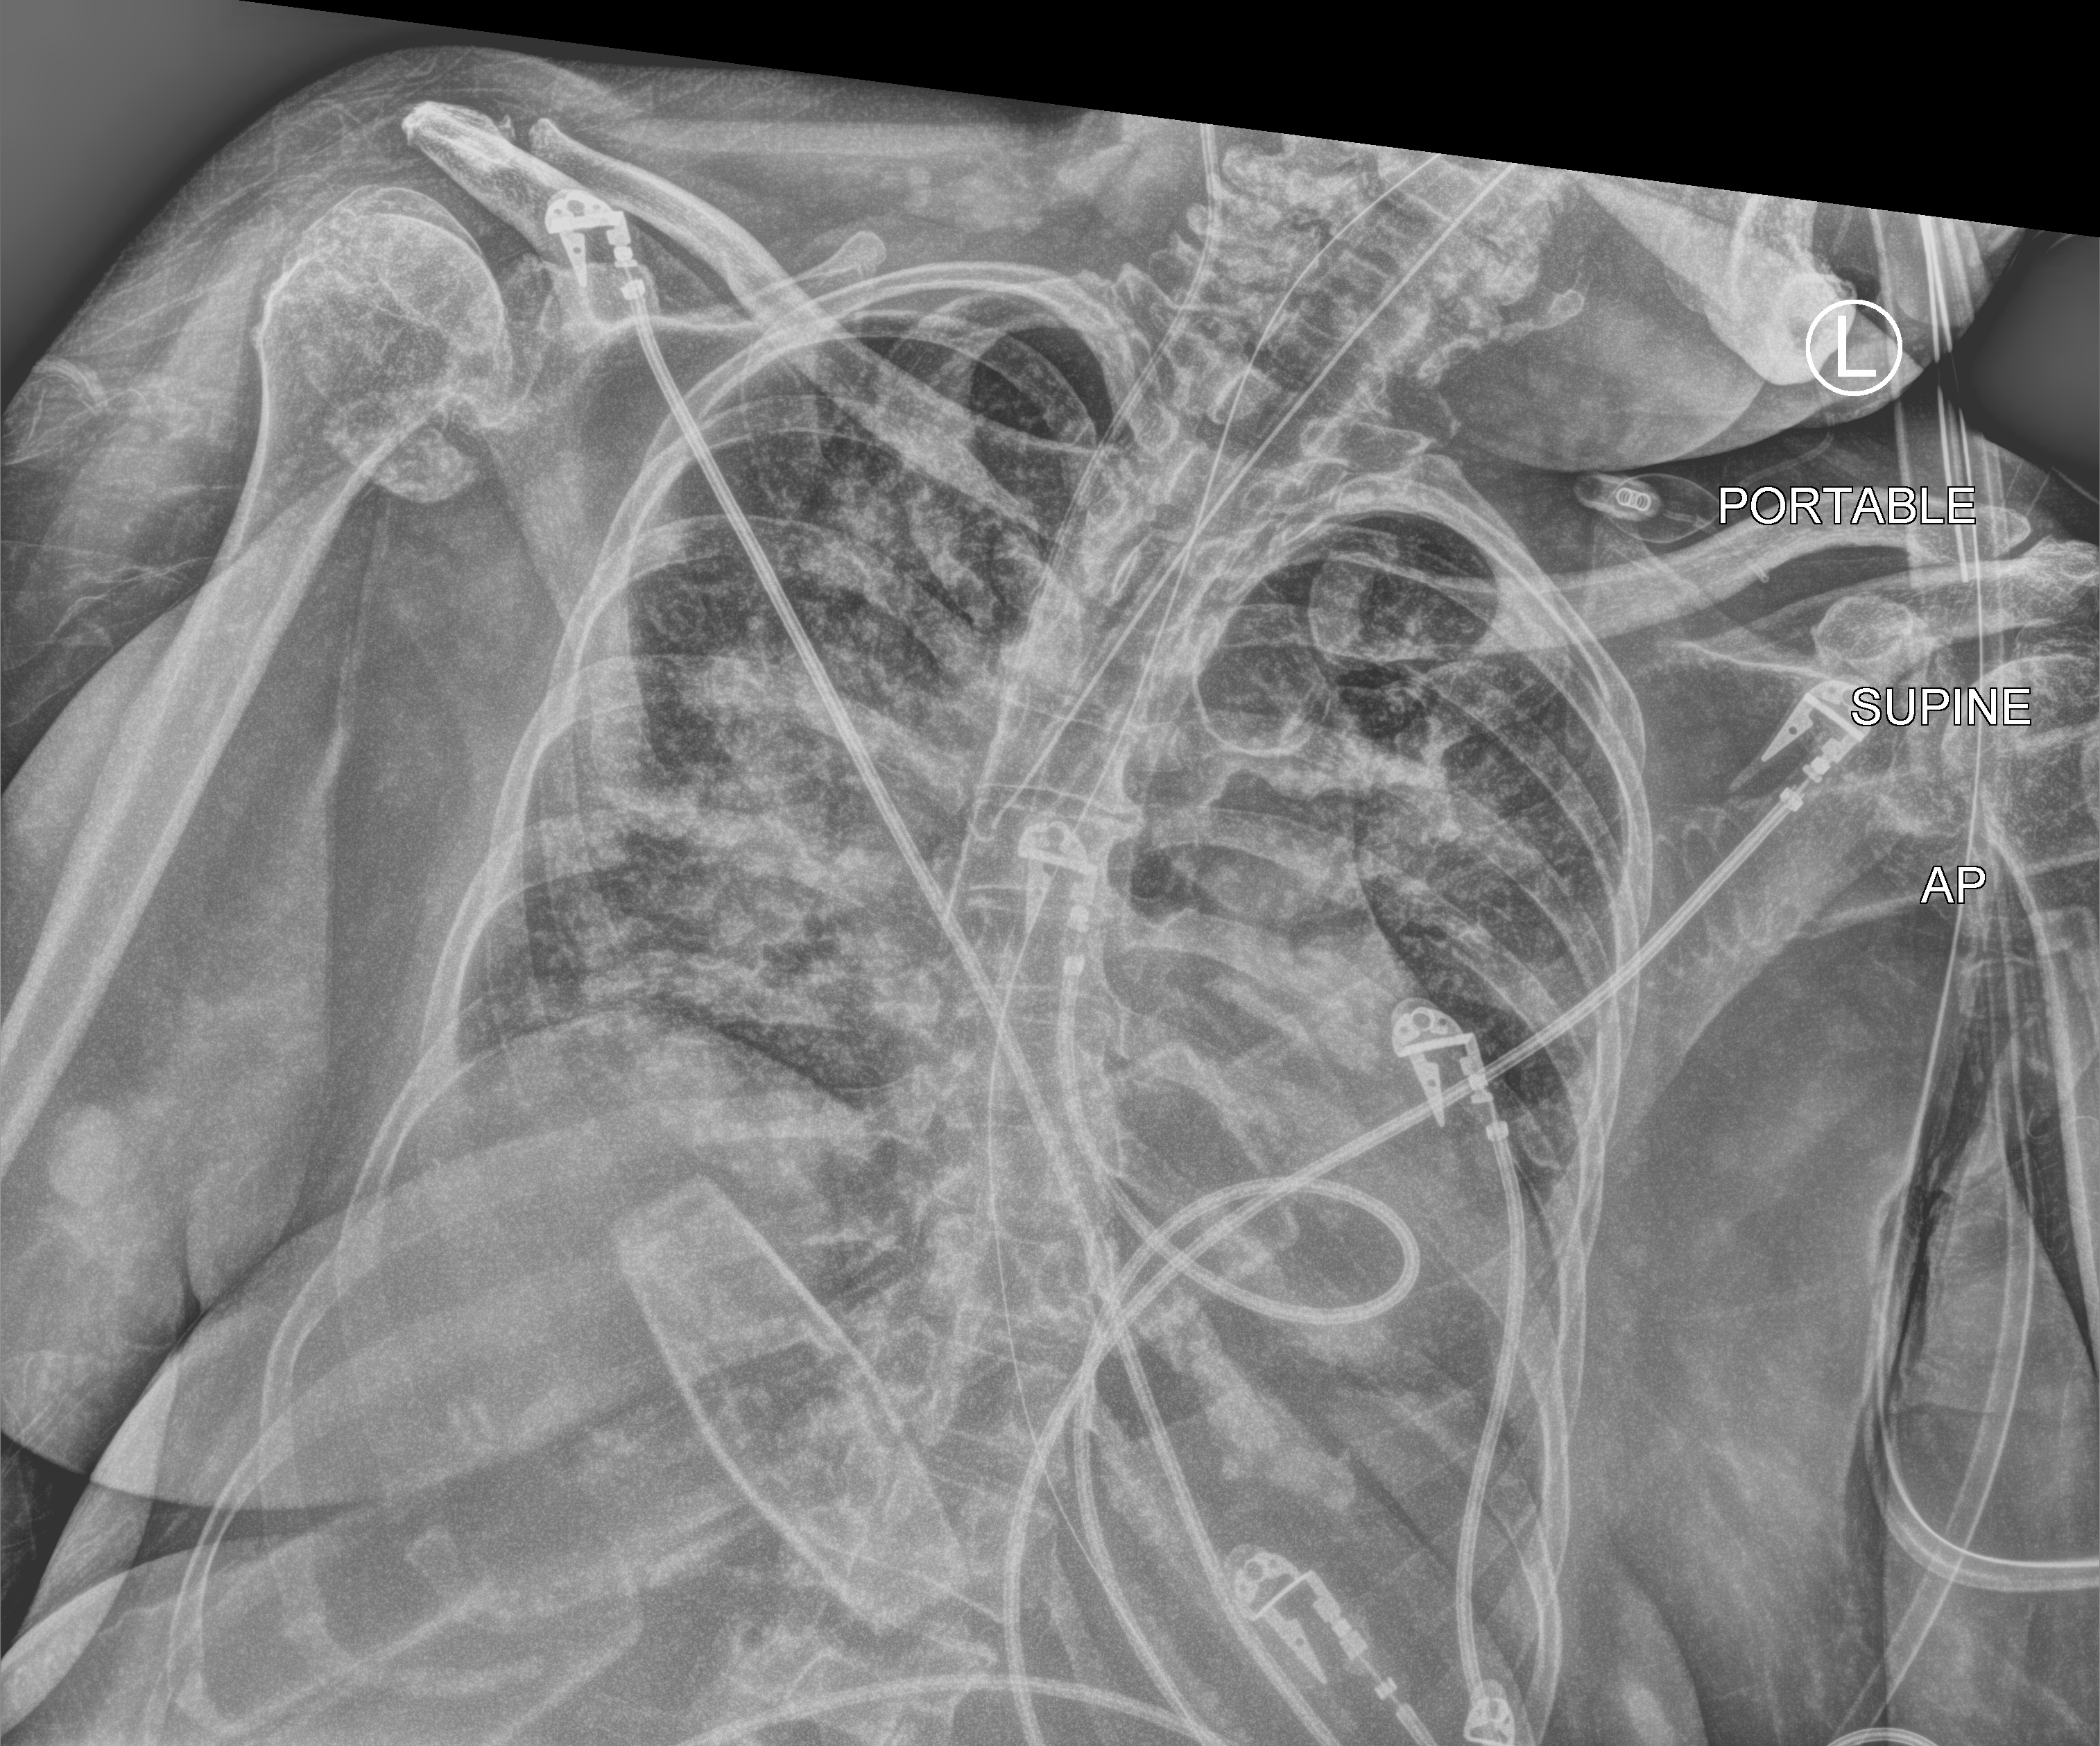
Chest X-ray (portable). Patient hospitalised with COVID-19; female, aged 60–74 years.
Admission-level facts for this patient (not findings on this image; timing relative to this image not recorded): admitted to intensive care during this hospital stay: yes; smoking status (admission record): never; mechanically ventilated during this hospital stay: yes.